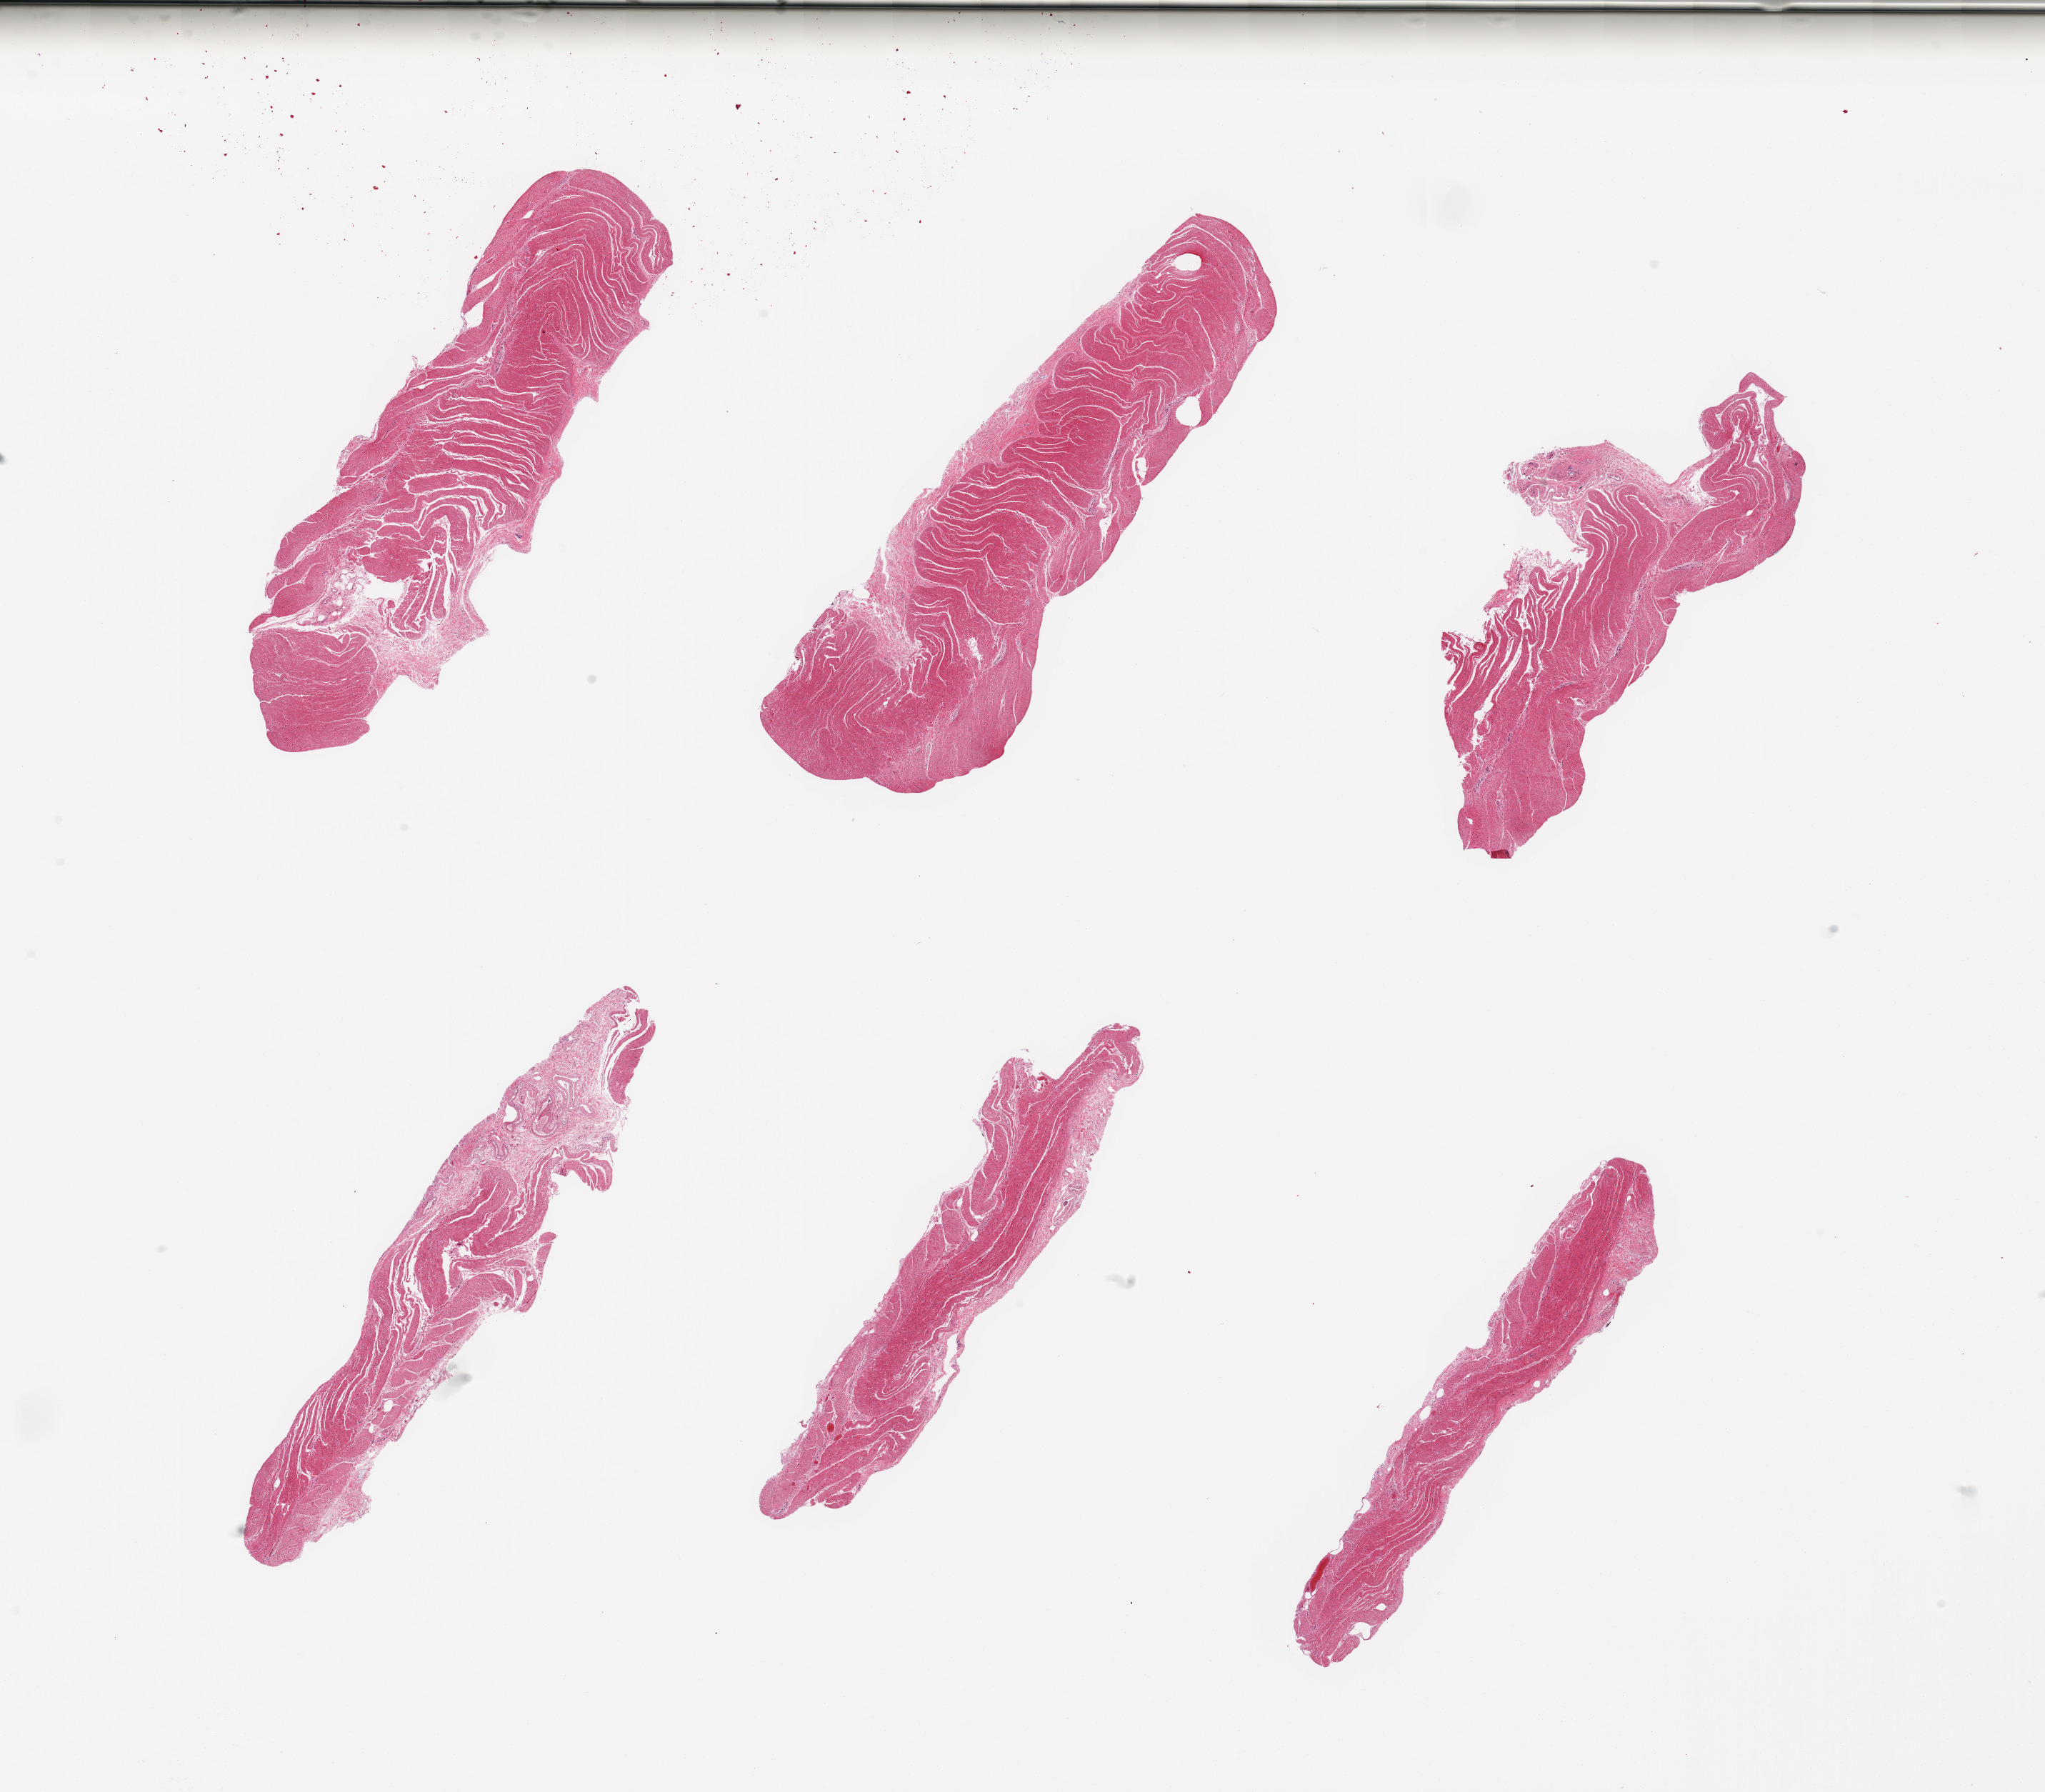
Whole-slide image, hematoxylin and eosin (H&E) stain — a low-resolution overview of the entire scanned area, about 22.6 x 19.8 mm; PAXgene-fixed, paraffin-embedded tissue; target tissue: sigmoid colon; donor tissue sample.
Pathologist's review note for this sample: 6 pieces; well dissected muscularis except for focal submucosal stroma.